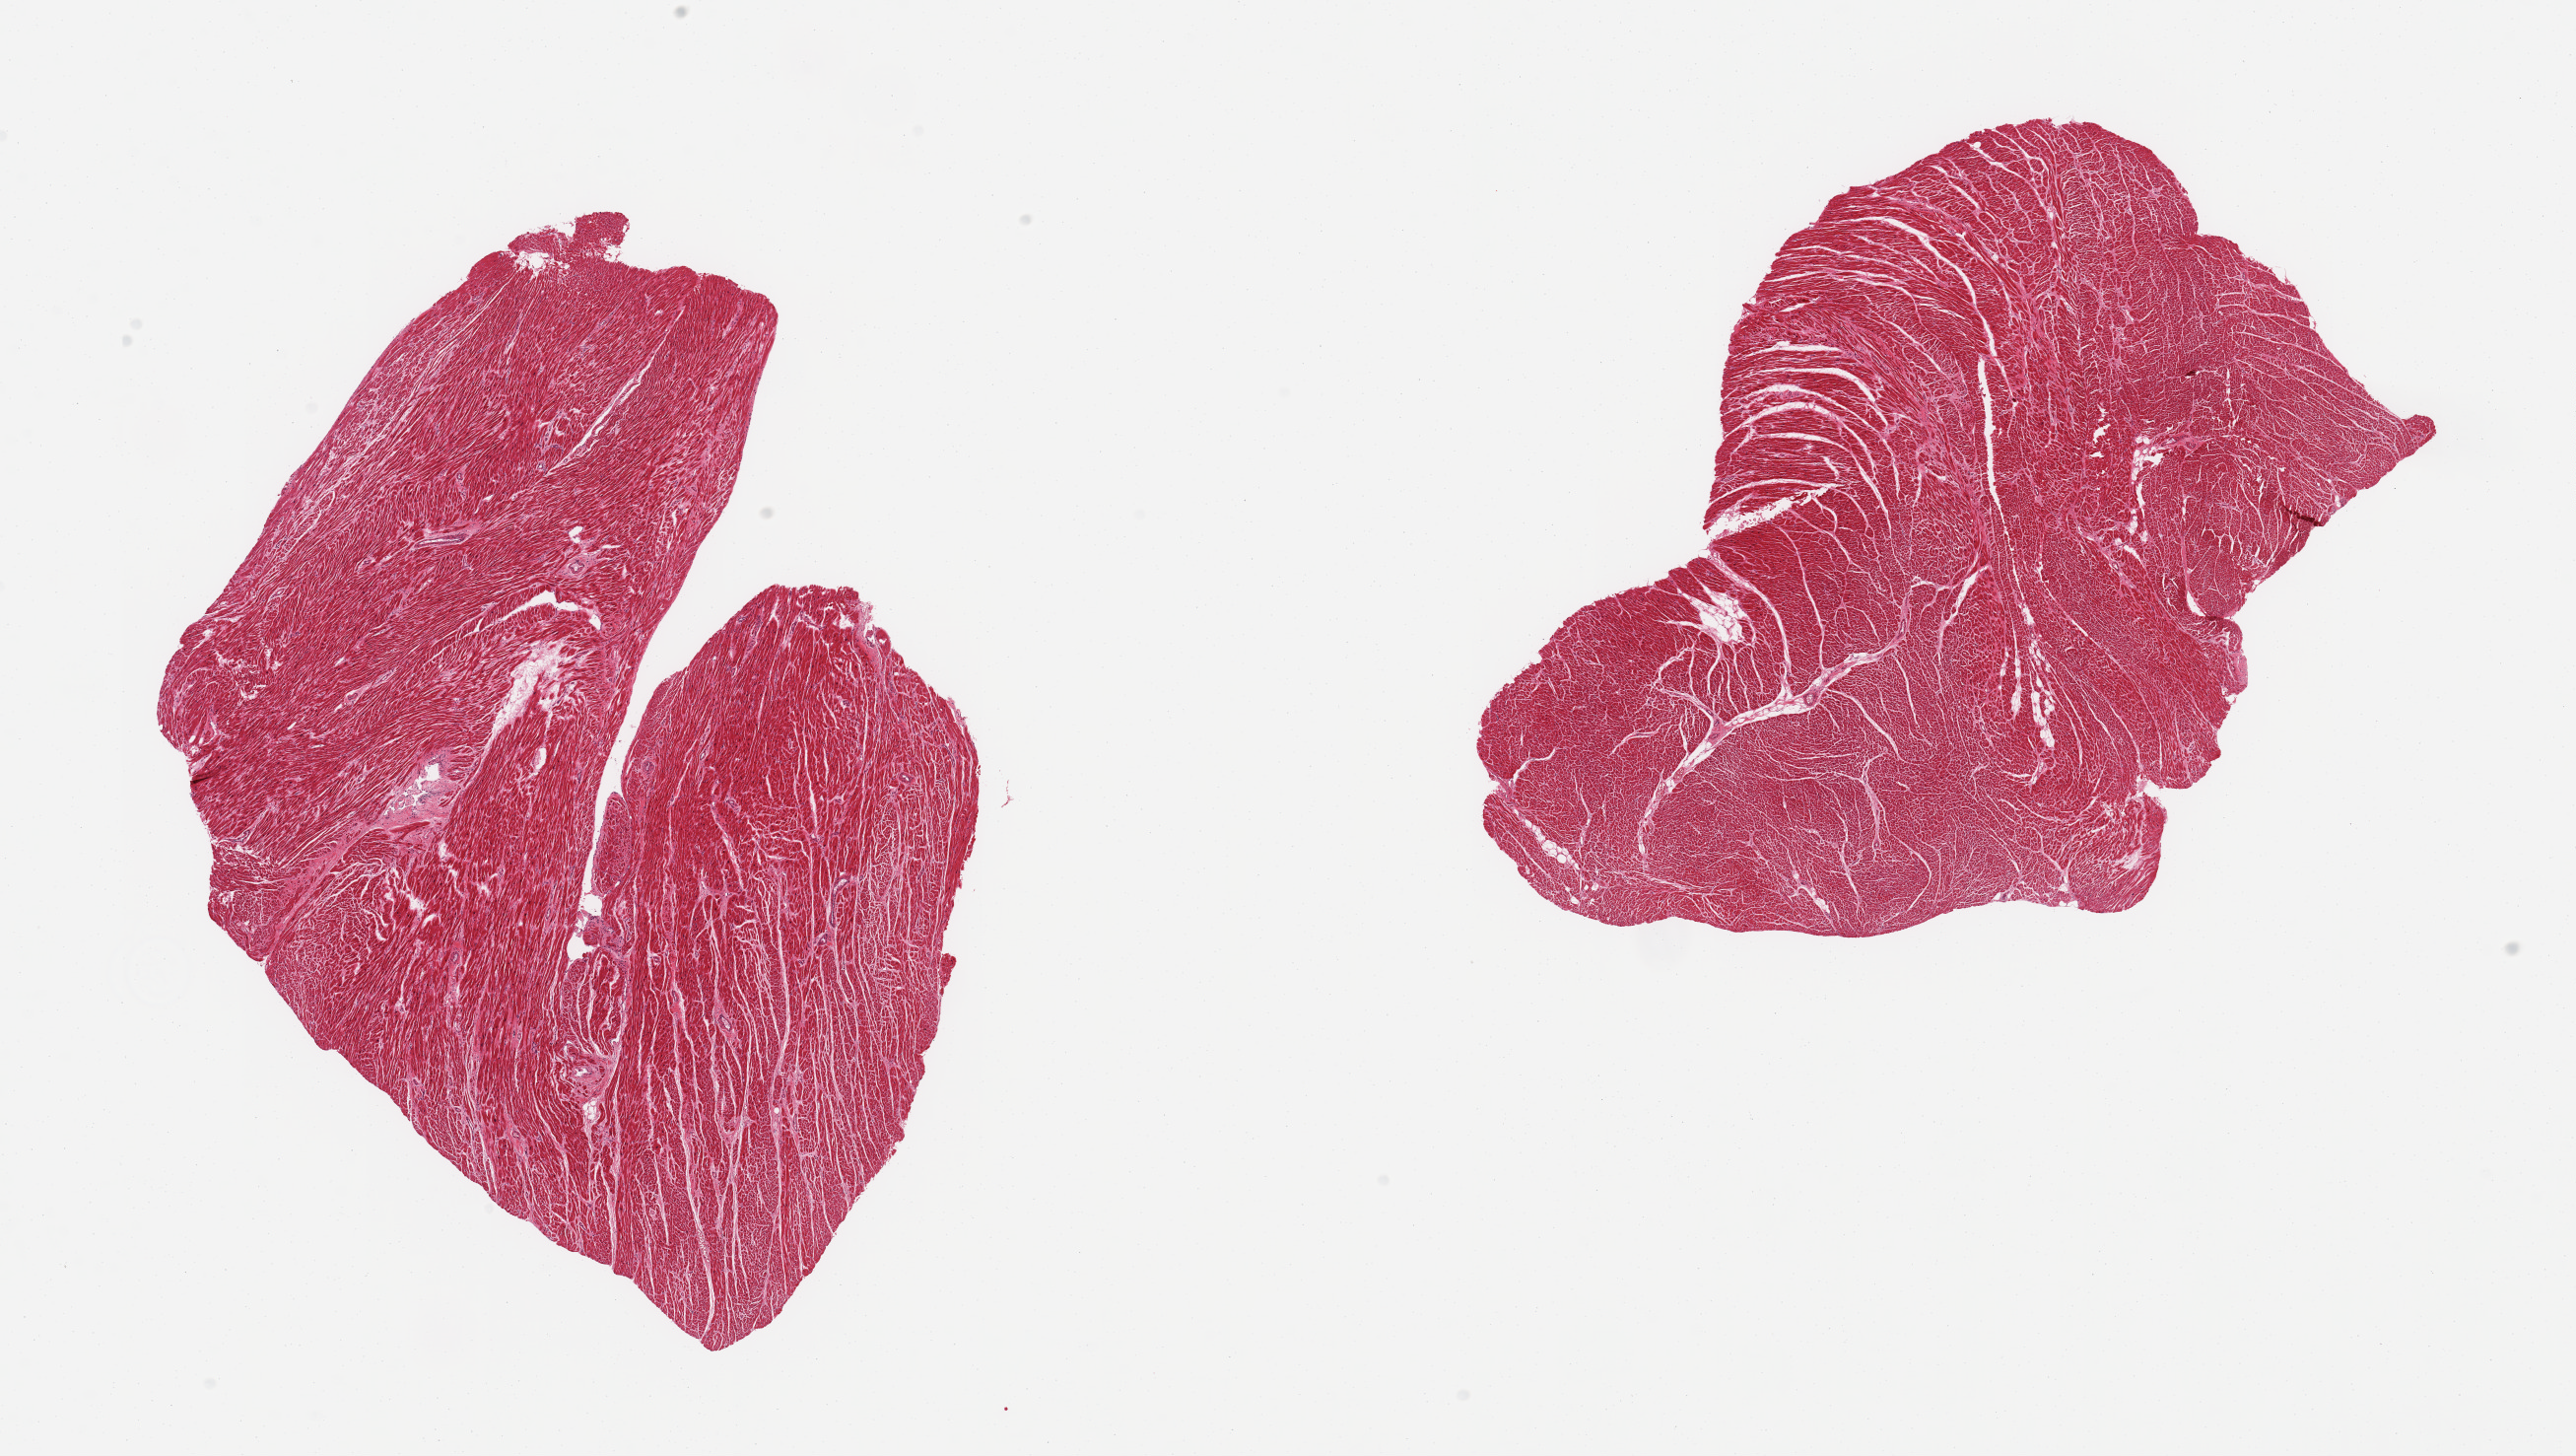
H&E whole-slide image, whole scanned area (about 20.7 x 11.7 mm) shown as a low-resolution overview, PAXgene-fixed paraffin-embedded (PFPE) section, section of heart (target tissue), tissue donor sample. Male donor.
Reviewer comment on this tissue sample: 2 pieces, moderate chronic ischemic changes/interstitial fibrosis.